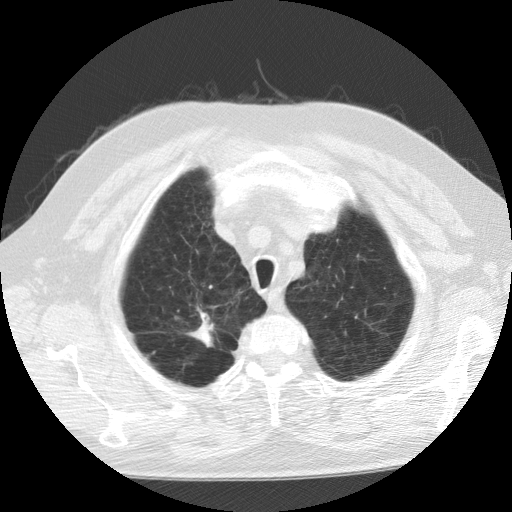
Low-dose screening chest CT, axial slice; second screening round (one year after baseline); lung window (W 1500 / L -600 HU); standard (soft-tissue) reconstruction kernel (STANDARD); slice 16 of 109 in the series; 512 × 512 image matrix. Male, age 64 years at enrolment. Current smoker at enrolment.
Expert reader's lesion annotation, bounding box (x1, y1, x2, y2) in pixels: (182, 313, 231, 359). The screening reader recorded 2 non-calcified nodules or masses ≥4 mm on this exam (left upper lobe, right lower lobe); which of them this box marks is not recorded. Official screen result: positive, other.